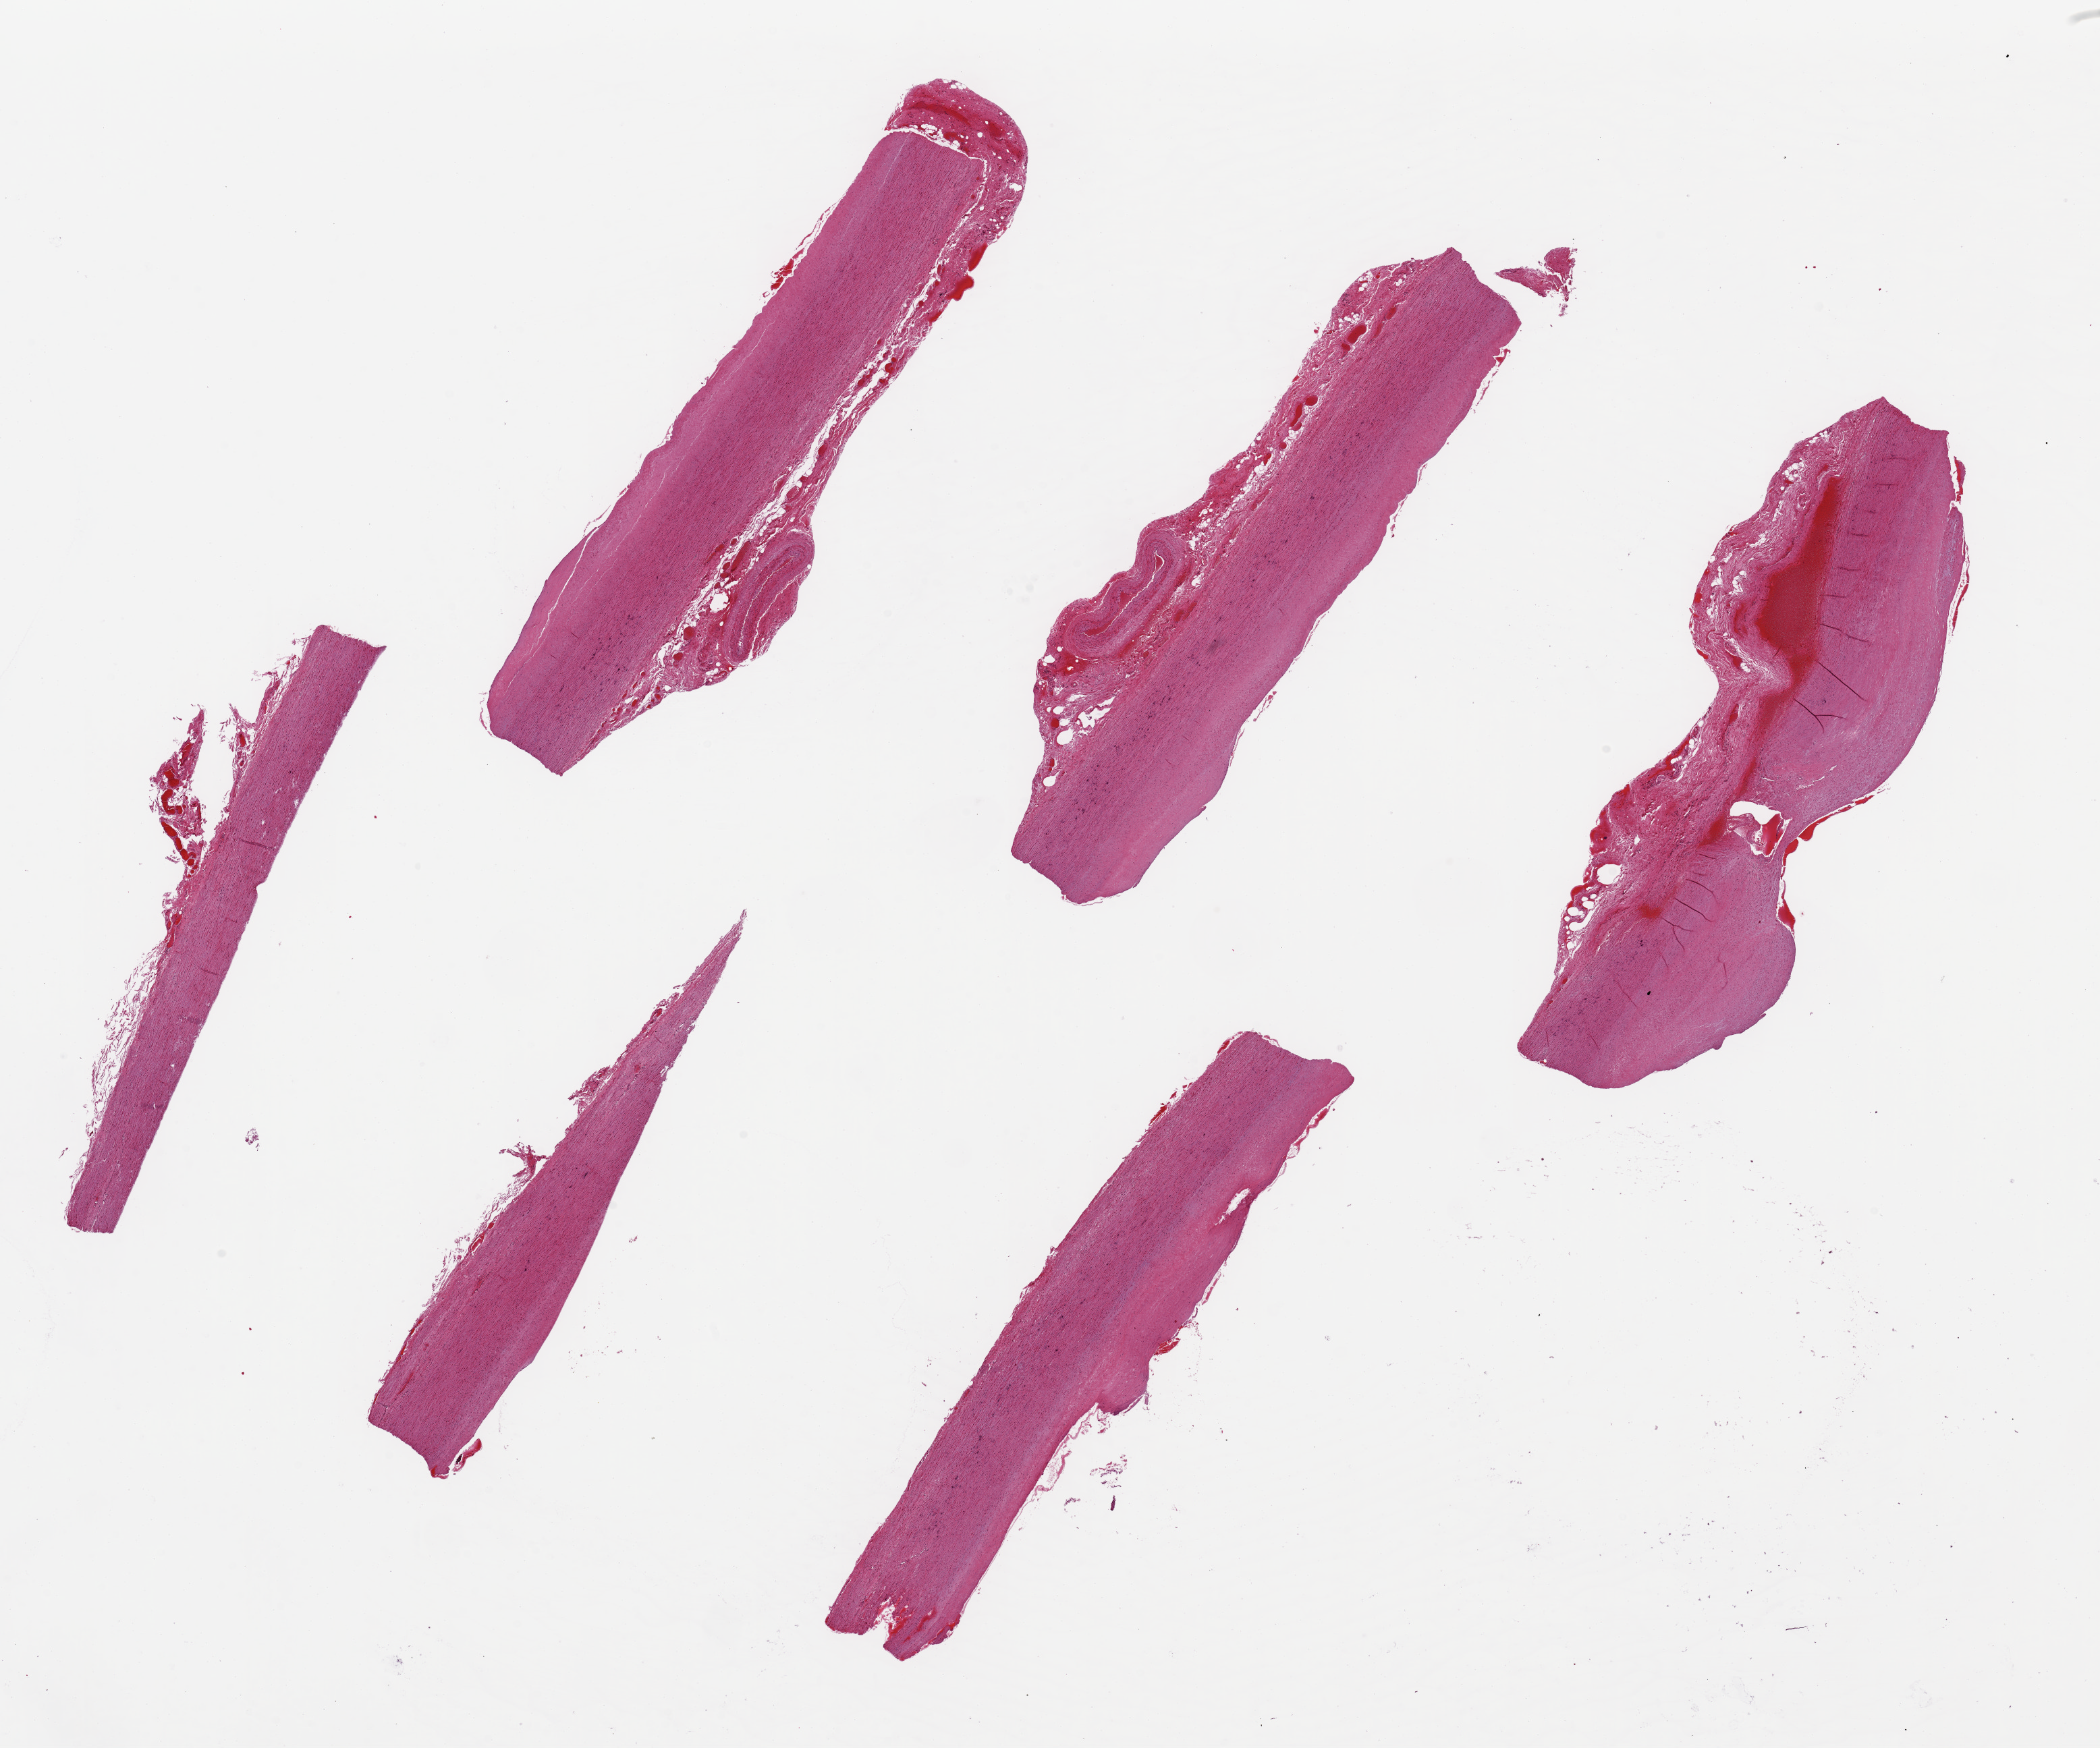
Hematoxylin and eosin (H&E) whole-slide image — a low-resolution overview of the entire scanned area, about 24.6 x 20.5 mm (acquisition: 20x scan); PAXgene-fixed paraffin-embedded (PFPE) section; target tissue: aorta; donor tissue sample. Donor: male.
- reviewer comment on this tissue sample: 6 pieces, ~9x2mm